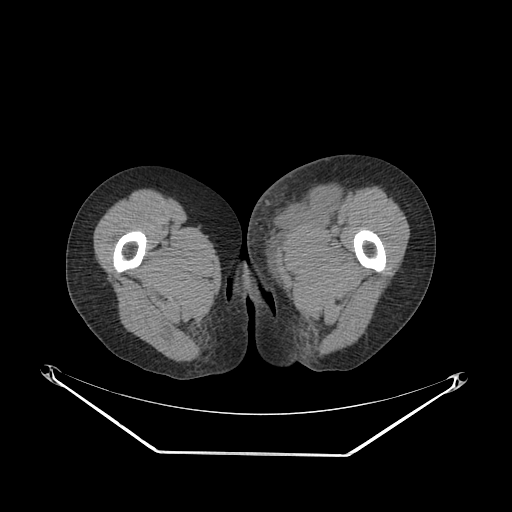
CT of an extremity soft-tissue mass (from a PET/CT study), one axial slice; position 46 of 267 along the scan axis; soft-tissue window (W 400 / L 40 HU); 512 × 512 image matrix. Female patient. Case-level facts recorded for this patient, not image findings: histological type: leiomyosarcoma; grade: high; site of the primary tumour: groin.
Structures marked on this image (expert contour drawn on MRI and transferred to this co-registered scan by the dataset authors):
- gross tumour volume including surrounding oedema: bounding box (x1, y1, x2, y2) in pixels: (247, 176, 339, 254)
- gross tumour volume (mass): (276, 185, 337, 223)